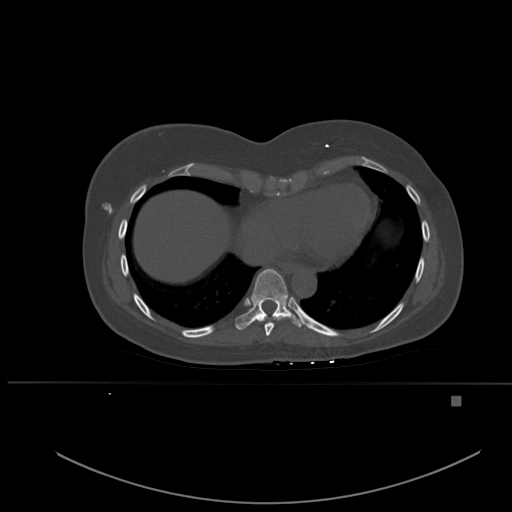
CT including the spine, one axial slice. Position 310 of 651 along the scan axis. Bone window (W 1800 / L 400 HU). 1.5 mm slice thickness. 512 × 512 image matrix, field of view 443 × 443 mm. Female patient, age 49 years. Case-level facts recorded for this patient, not image findings: primary cancer: breast; vertebrae with lytic lesions (as recorded): L3, T12, L4.
Outlined on this slice (semi-automatic segmentation, software-assisted and operator-edited):
- T8 vertebra: box from (x=262, y=320) to (x=275, y=336) px
- T9 vertebra: (x=235, y=269)–(x=301, y=330)